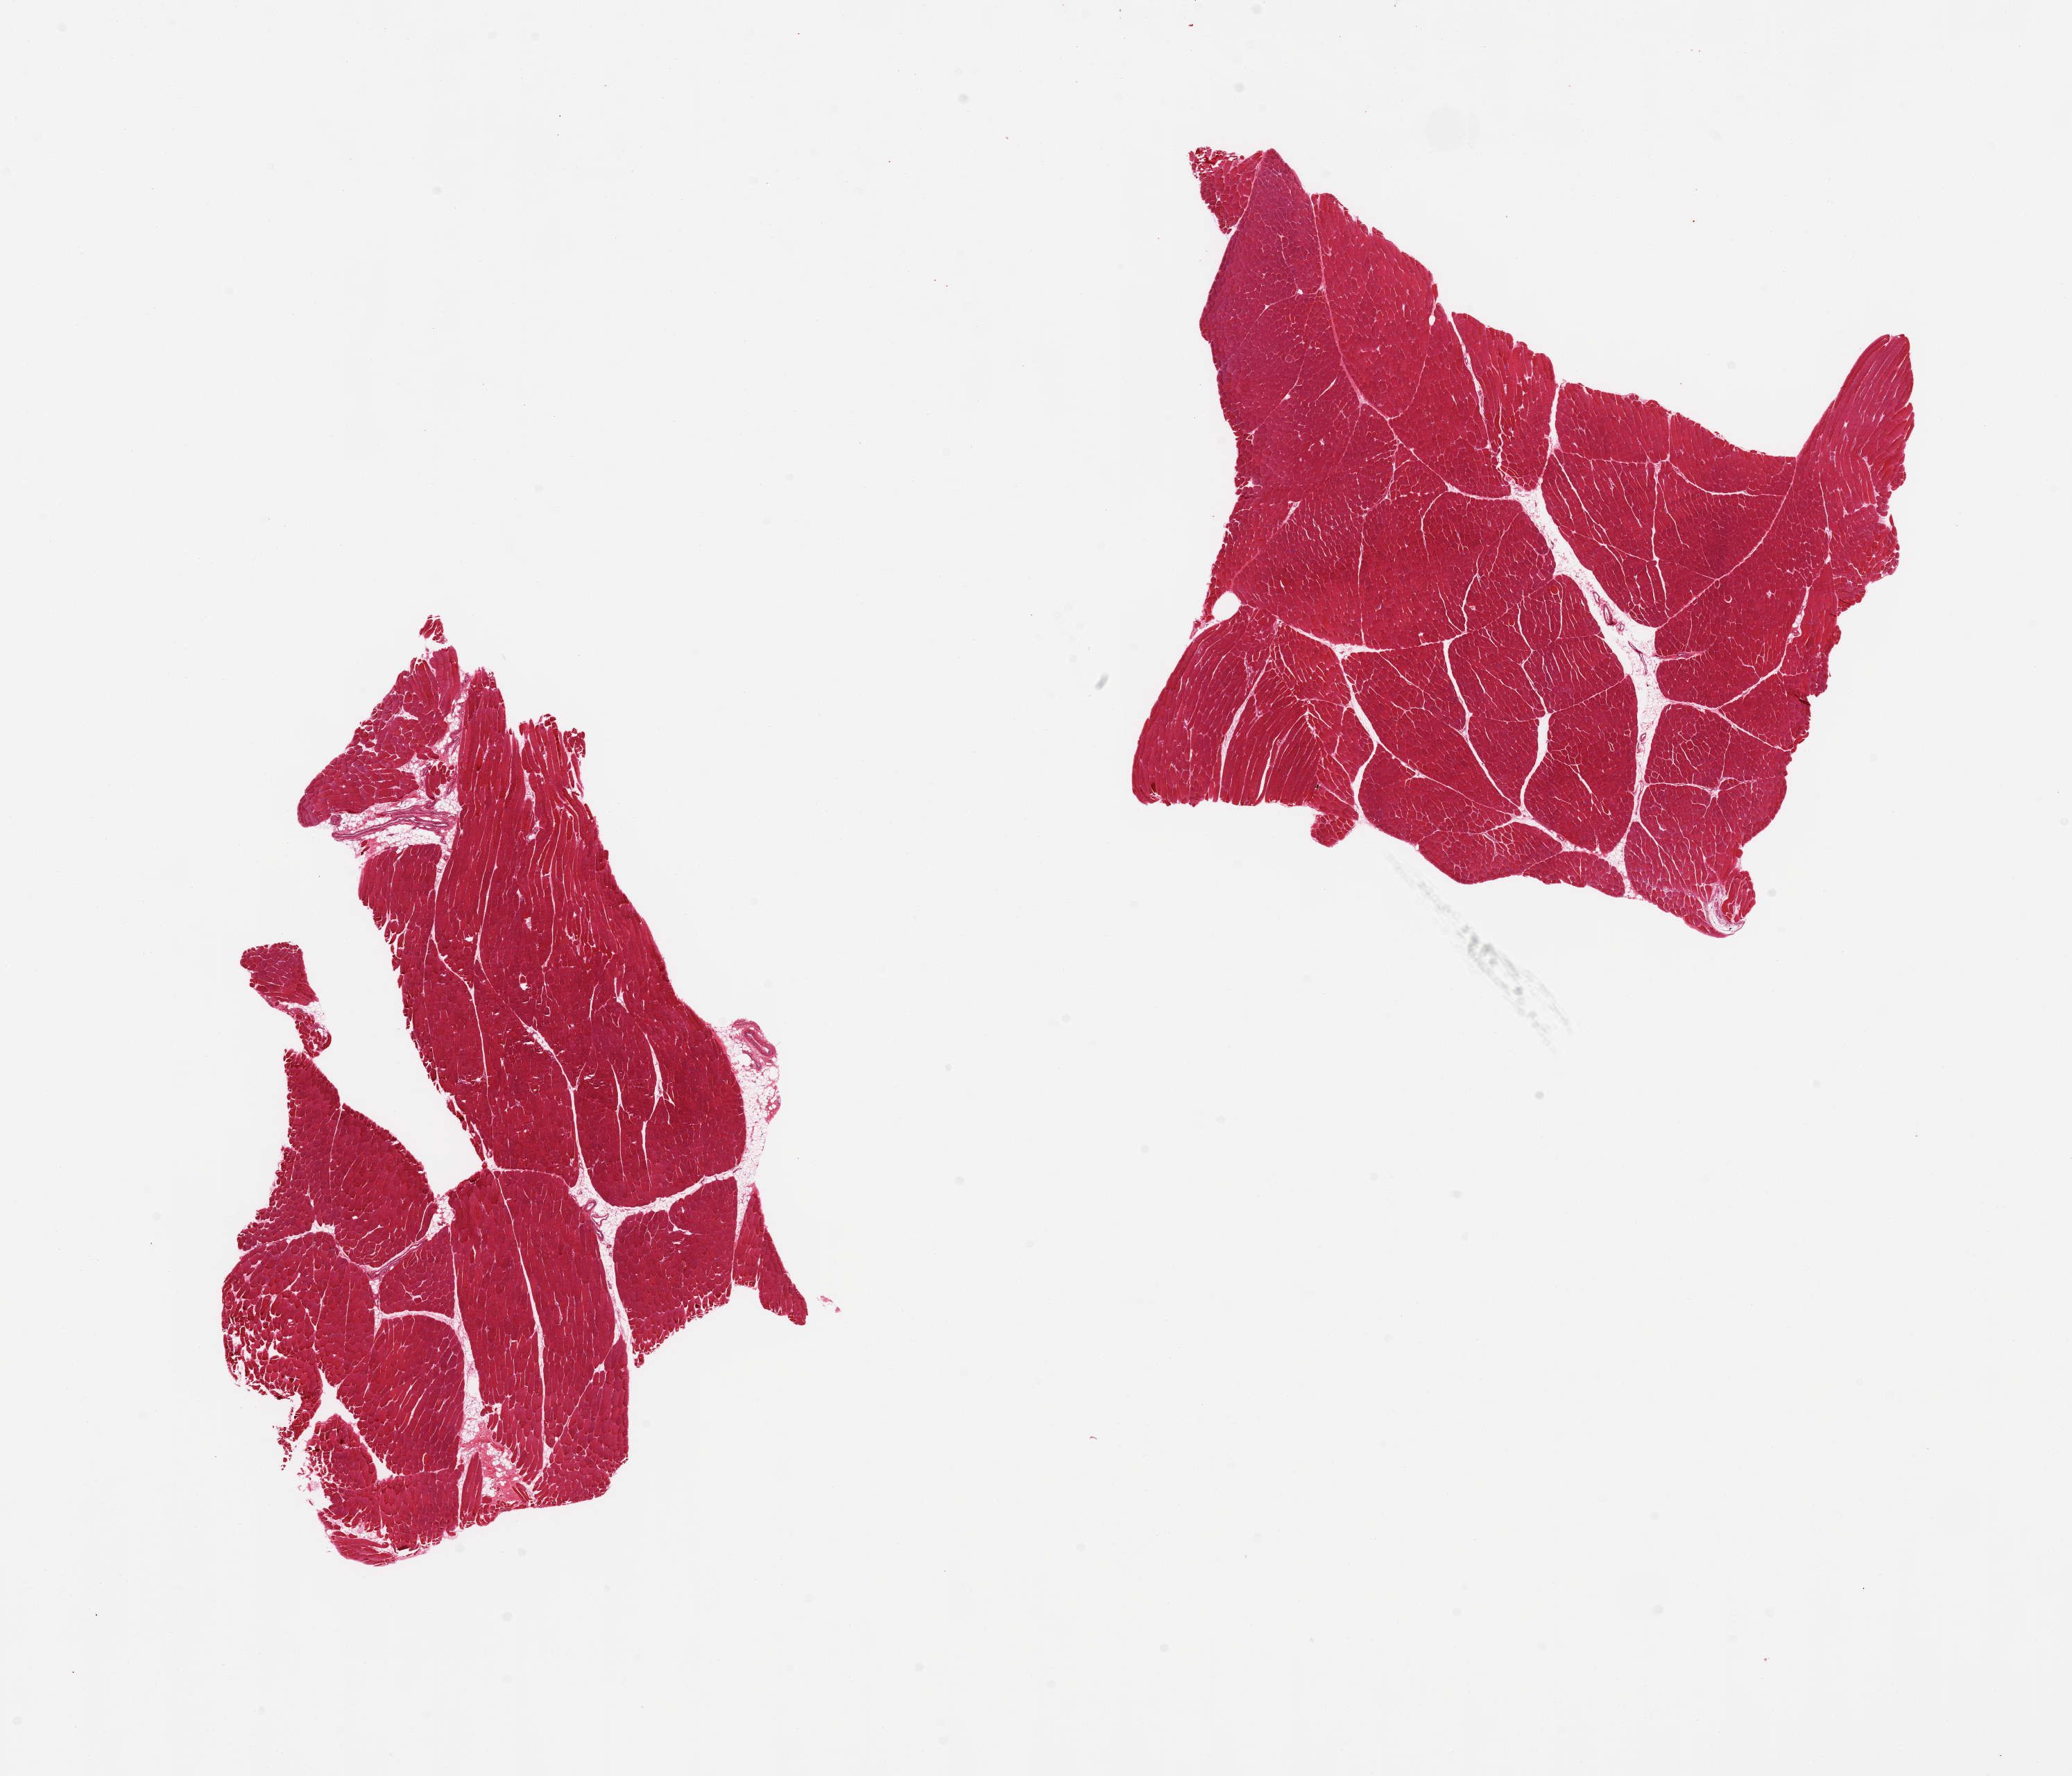
Whole-slide image, H&E stain, shown as a low-resolution overview of the whole scanned area (about 23.6 x 20.2 mm, acquisition: 20x scan). PAXgene-fixed, paraffin-embedded tissue. Section of skeletal muscle (target tissue). Donor tissue sample. Male donor.
* pathologist's review note for this sample: 2 pieces, fewfoci of interstiital fat